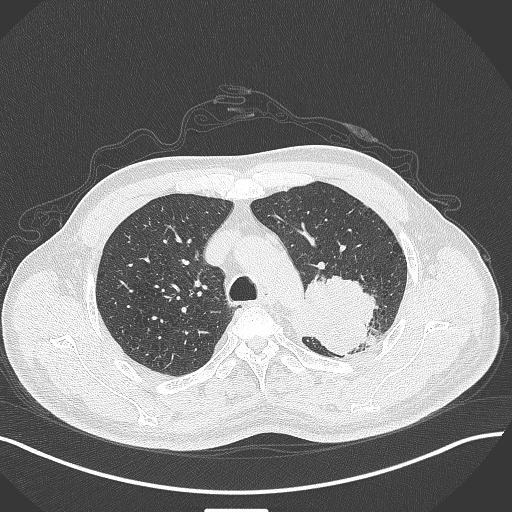
Chest CT, one axial slice; position 321 of 429 along the scan axis; reconstruction kernel B70f; 120 kVp; lung window (W 1500 / L -600 HU); 1 mm slice thickness; 512 × 512 image matrix, field of view 400 × 400 mm. Patient: male, 55 years. From the clinical record (not read from this slice): clinical TNM (as recorded): T3 N0 M1c; histopathological grade: G3.
Outlined on this slice (rectangle marked by the reading radiologist):
- lung tumour (recorded histology: adenocarcinoma): bounding box [x1, y1, x2, y2] px = [287, 263, 378, 357]